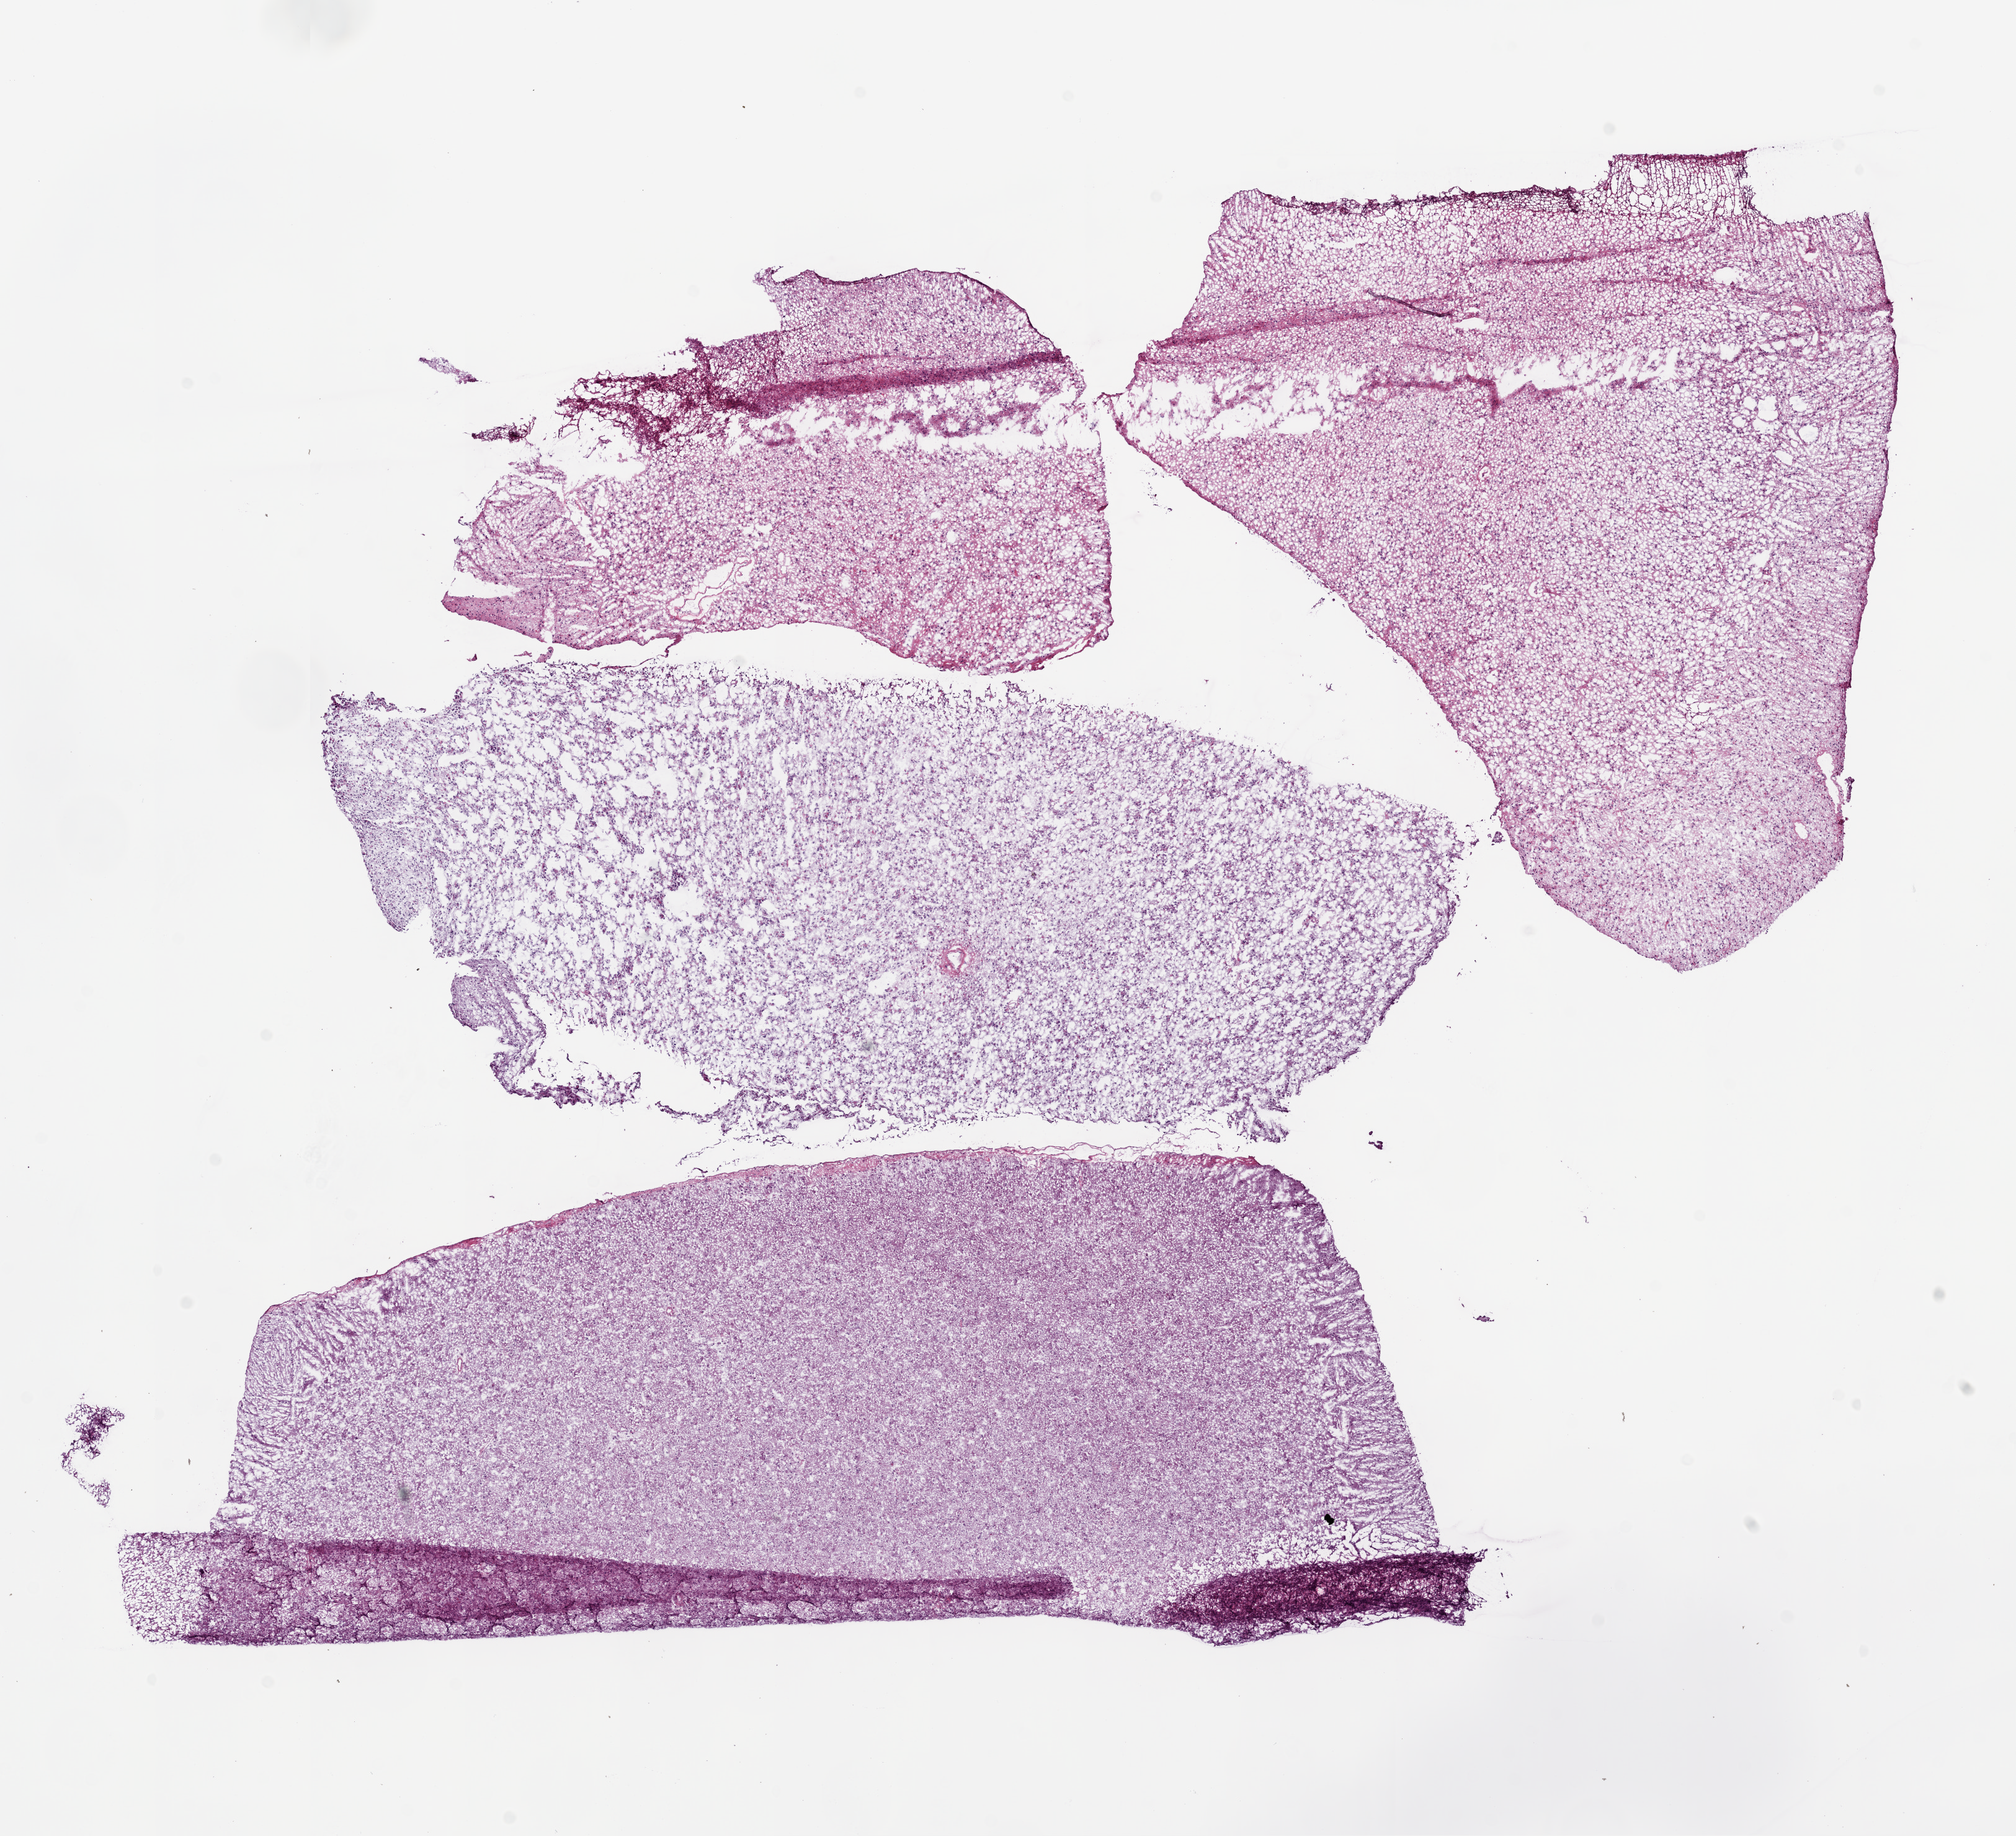
Digitized H&E tissue section (whole slide) — shown as a low-resolution overview of the whole scanned area (about 13.0 x 11.9 mm, acquisition: 20x scan); frozen section from the bottom of the tissue portion; primary tumour sample from the brain. Patient: female, age at initial diagnosis 62 years. Histologic grade: G3 (poorly differentiated). Composition of this section per pathologist review: tumour cells 100%, tumour nuclei 65%, normal cells 0%, stromal cells 0%, necrosis 0%.
Diagnosis: Astrocytoma, anaplastic.